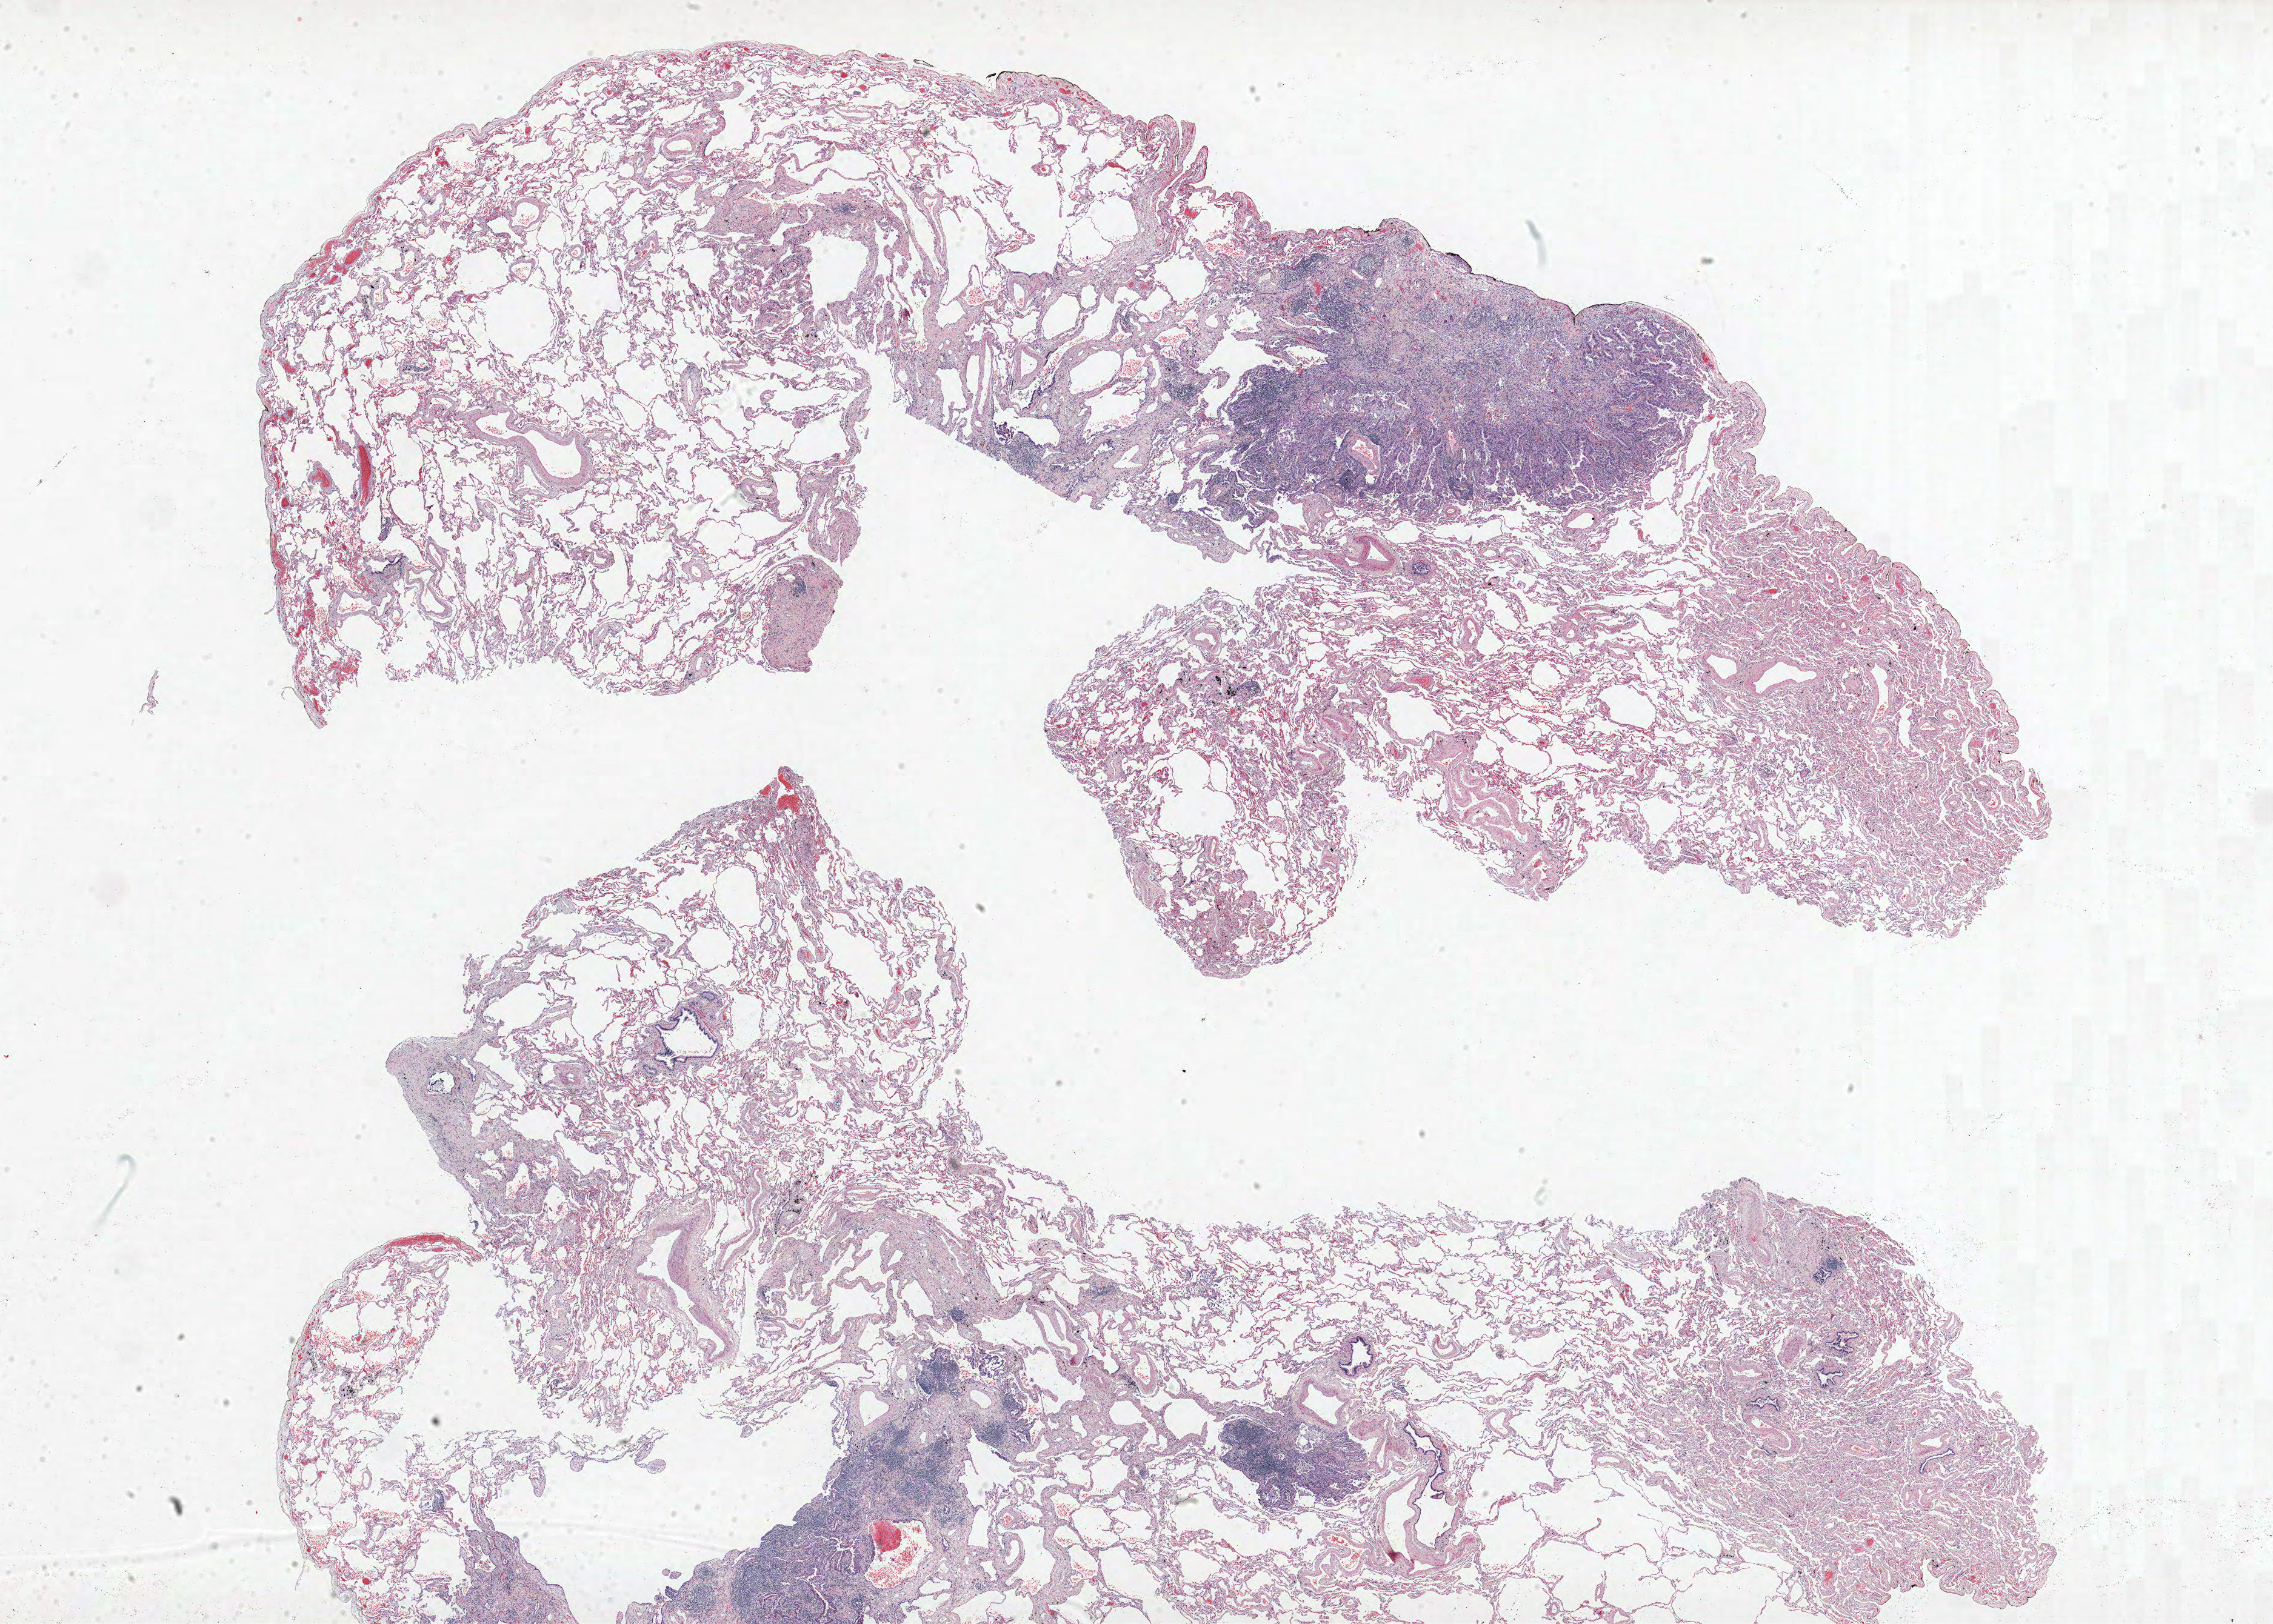
H&E-stained whole-slide image, low-resolution overview of the scanned area, about 30.0 x 21.4 mm (acquisition: 40x scan); FFPE section; lung tissue. Female, age 59 at enrolment. Grade: moderately differentiated (G2).
Stage (AJCC 6th edition): IIIB. Participant's lung-cancer diagnosis: Adenocarcinoma, NOS. Primary tumour location (clinical record): left lower lobe.